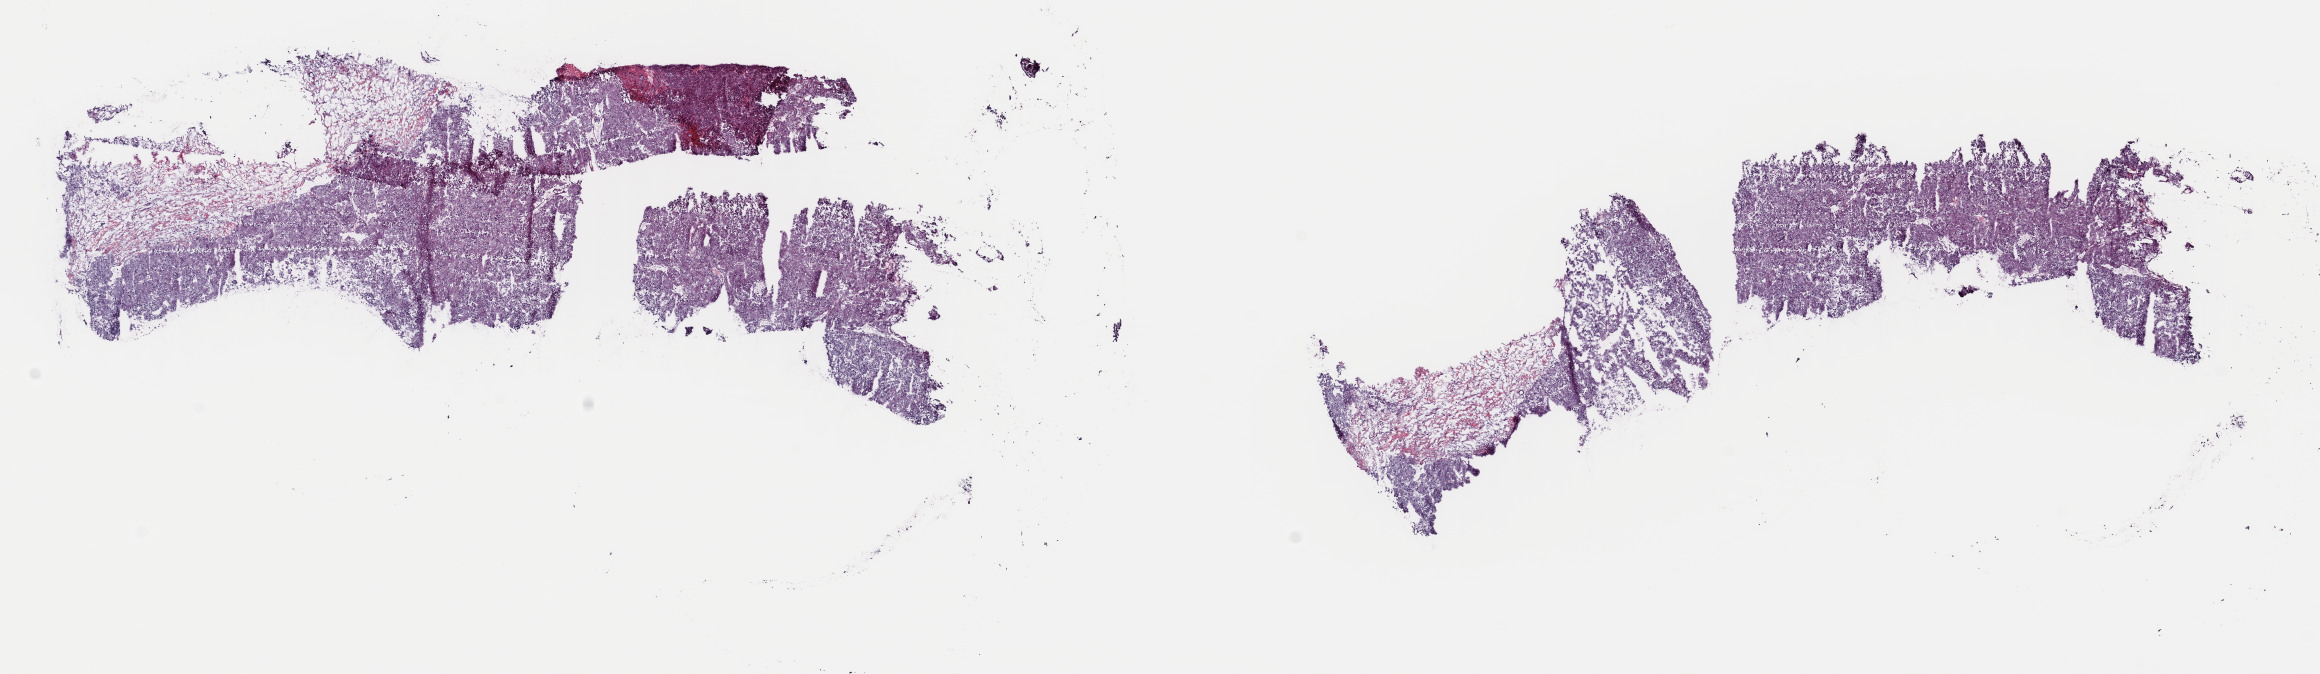
H&E whole-slide image, shown as a low-resolution overview of the whole scanned area (about 18.3 x 5.3 mm), frozen section, kidney, primary tumour sample. Male, age 71 years at initial diagnosis. Composition of this section per pathologist review: tumour cells 80%, tumour nuclei 80%, normal cells 0%, stromal cells 20%, necrosis 0%. Inflammatory infiltration, as recorded: lymphocyte infiltration 2%, monocyte infiltration 3%, neutrophil infiltration 1%.
Diagnosis: Papillary adenocarcinoma, NOS. AJCC pathologic stage: III (7th edition).